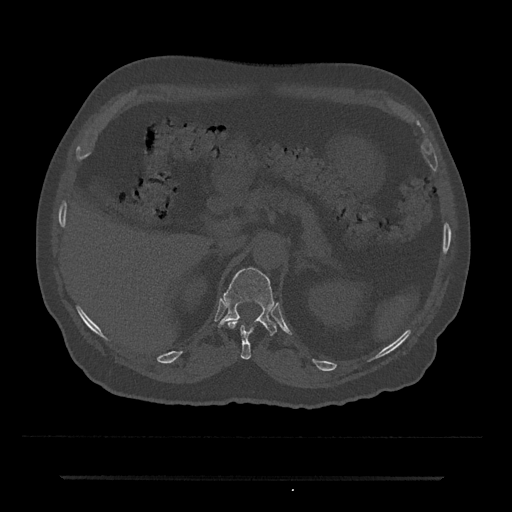
CT including the spine, one axial slice. Slice 145 of 797 in the series (ordered by position). Reconstruction kernel Br40s/3. 120 kVp. Bone window (W 1800 / L 400 HU). 0.5 mm slice thickness. 512 × 512 image matrix, field of view 437 × 437 mm. Patient: male, 69 years. From the clinical record (not read from this slice): primary cancer: prostate.
Structures marked on this image (semi-automatic segmentation, software-assisted and operator-edited):
- T11 vertebra: bounding box [x1, y1, x2, y2] px = [227, 321, 254, 360]
- T12 vertebra: [217, 267, 277, 336]